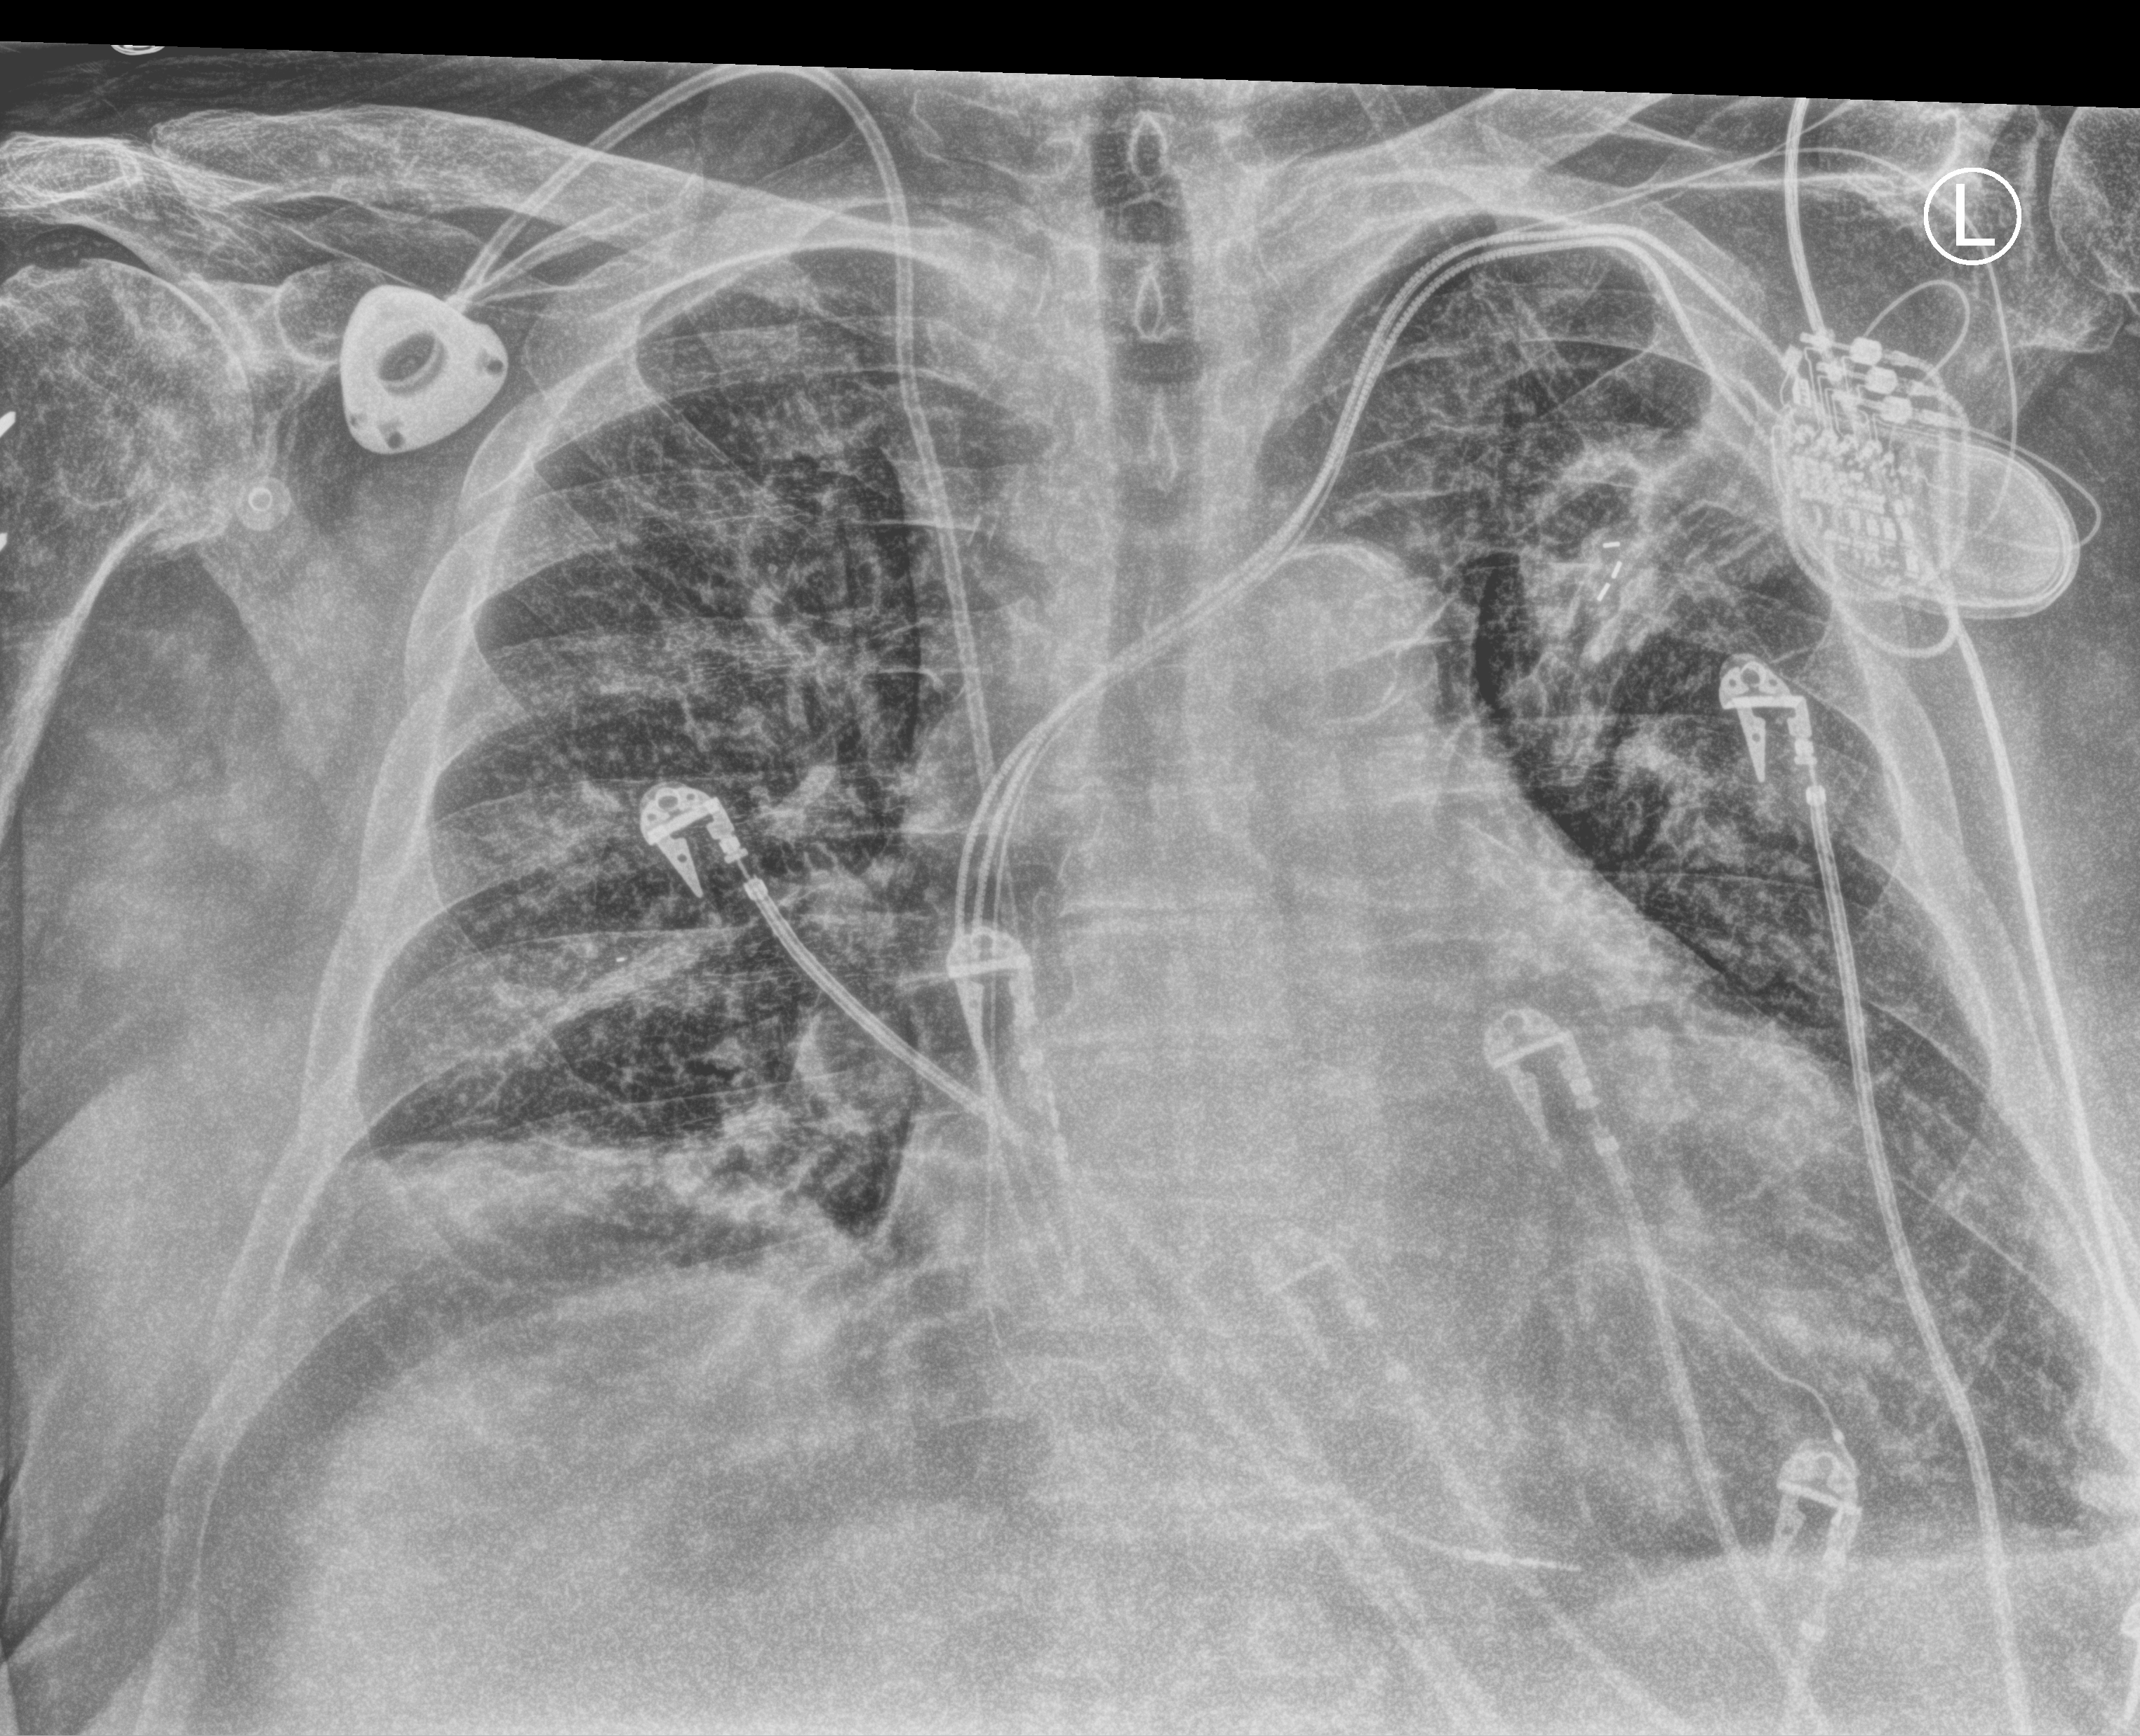
Portable chest radiograph. Male patient hospitalised with COVID-19, age 60–74 years.
From the hospital-stay record, not from the radiograph (when in the stay this image was taken is not recorded): mechanically ventilated during this hospital stay: no; admitted to intensive care during this hospital stay: yes; length of hospital stay: 20 days.